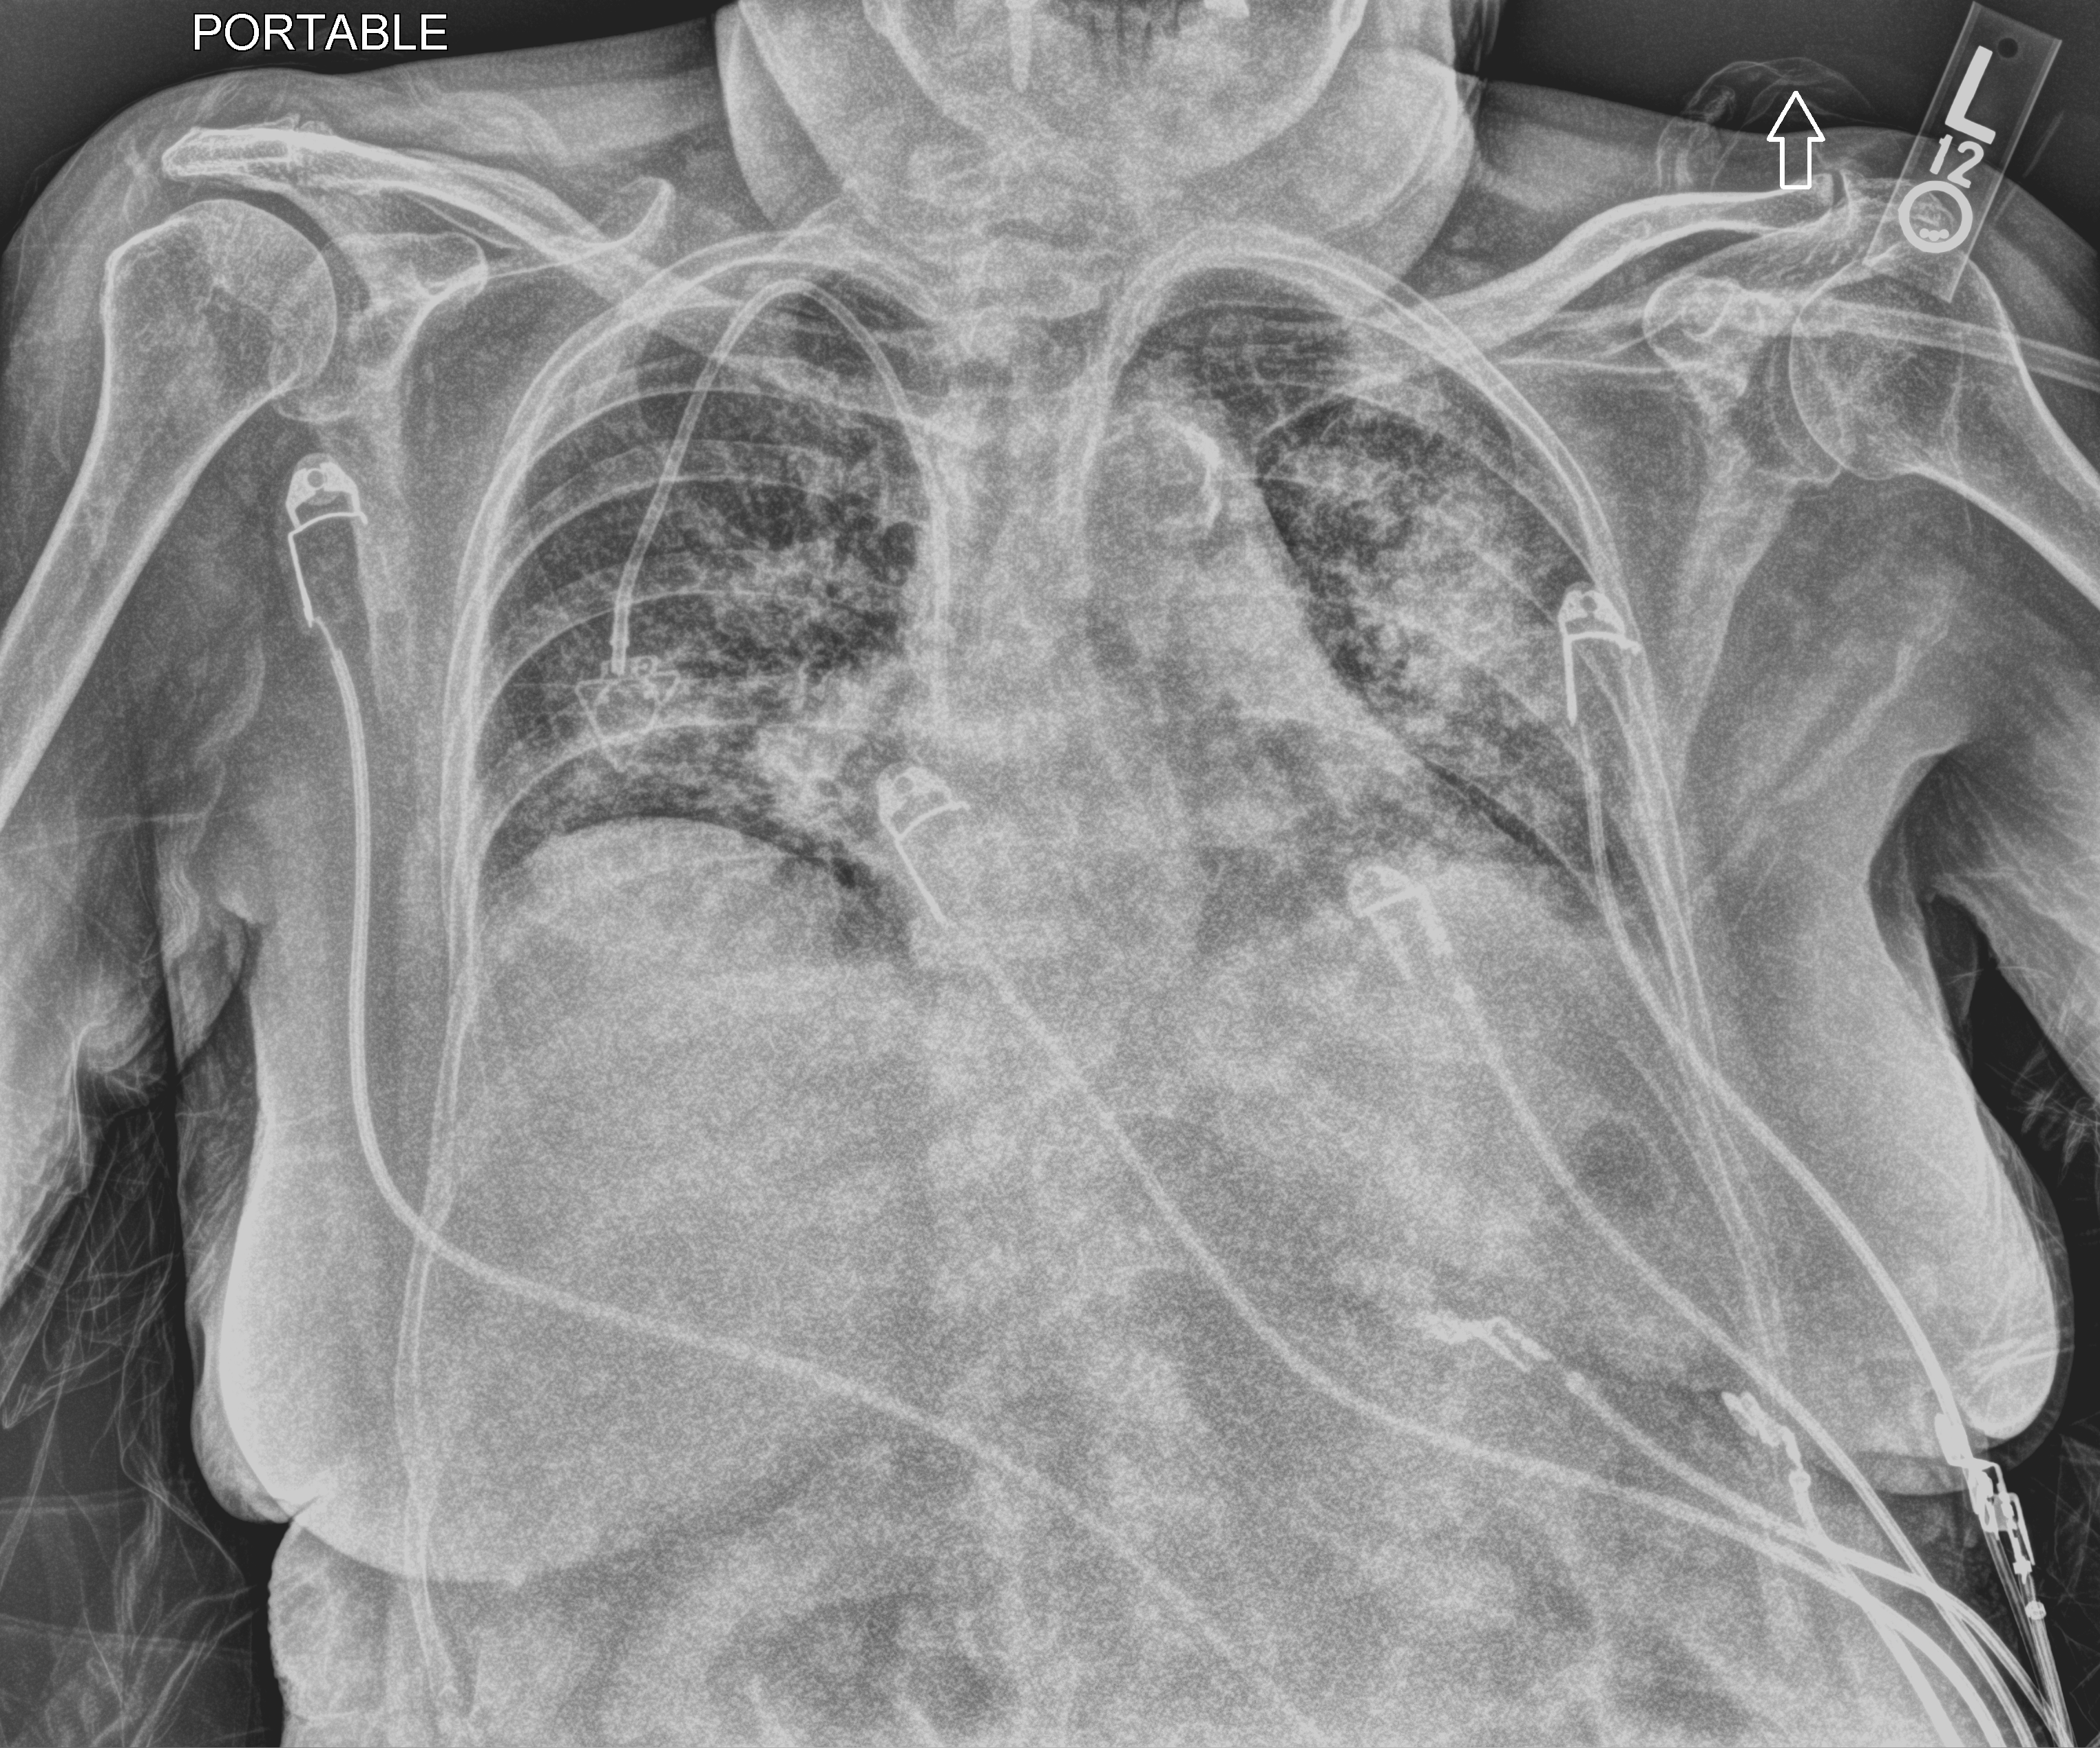
Portable chest radiograph. Female patient hospitalised with COVID-19, age 75–90 years.
Admission-level facts for this patient (not findings on this image; timing relative to this image not recorded):
- admitted to intensive care during this hospital stay: no